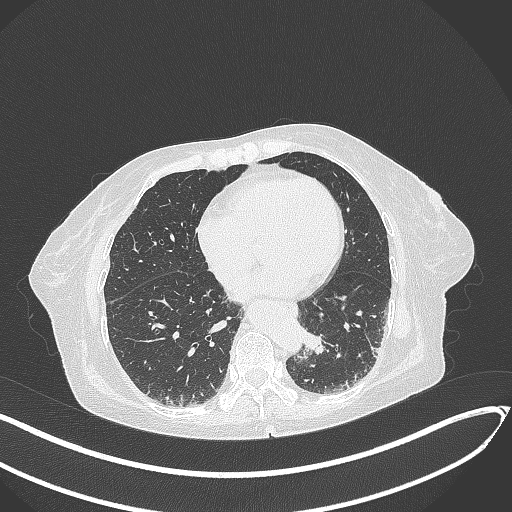
Chest CT, one axial slice. Slice 75 of 324 in the series (ordered by position). Reconstruction kernel B70f. 120 kVp. Lung window (W 1500 / L -600 HU). 1 mm slice thickness. 512 × 512 image matrix, field of view 400 × 400 mm. Female patient, age 82 years. Case-level facts recorded for this patient, not image findings: clinical TNM (as recorded): T1b N0 M1.
Outlined on this slice (bounding box drawn by a radiologist):
- lung tumour (recorded histology: adenocarcinoma): bounding box [x1, y1, x2, y2] px = [301, 327, 334, 359]